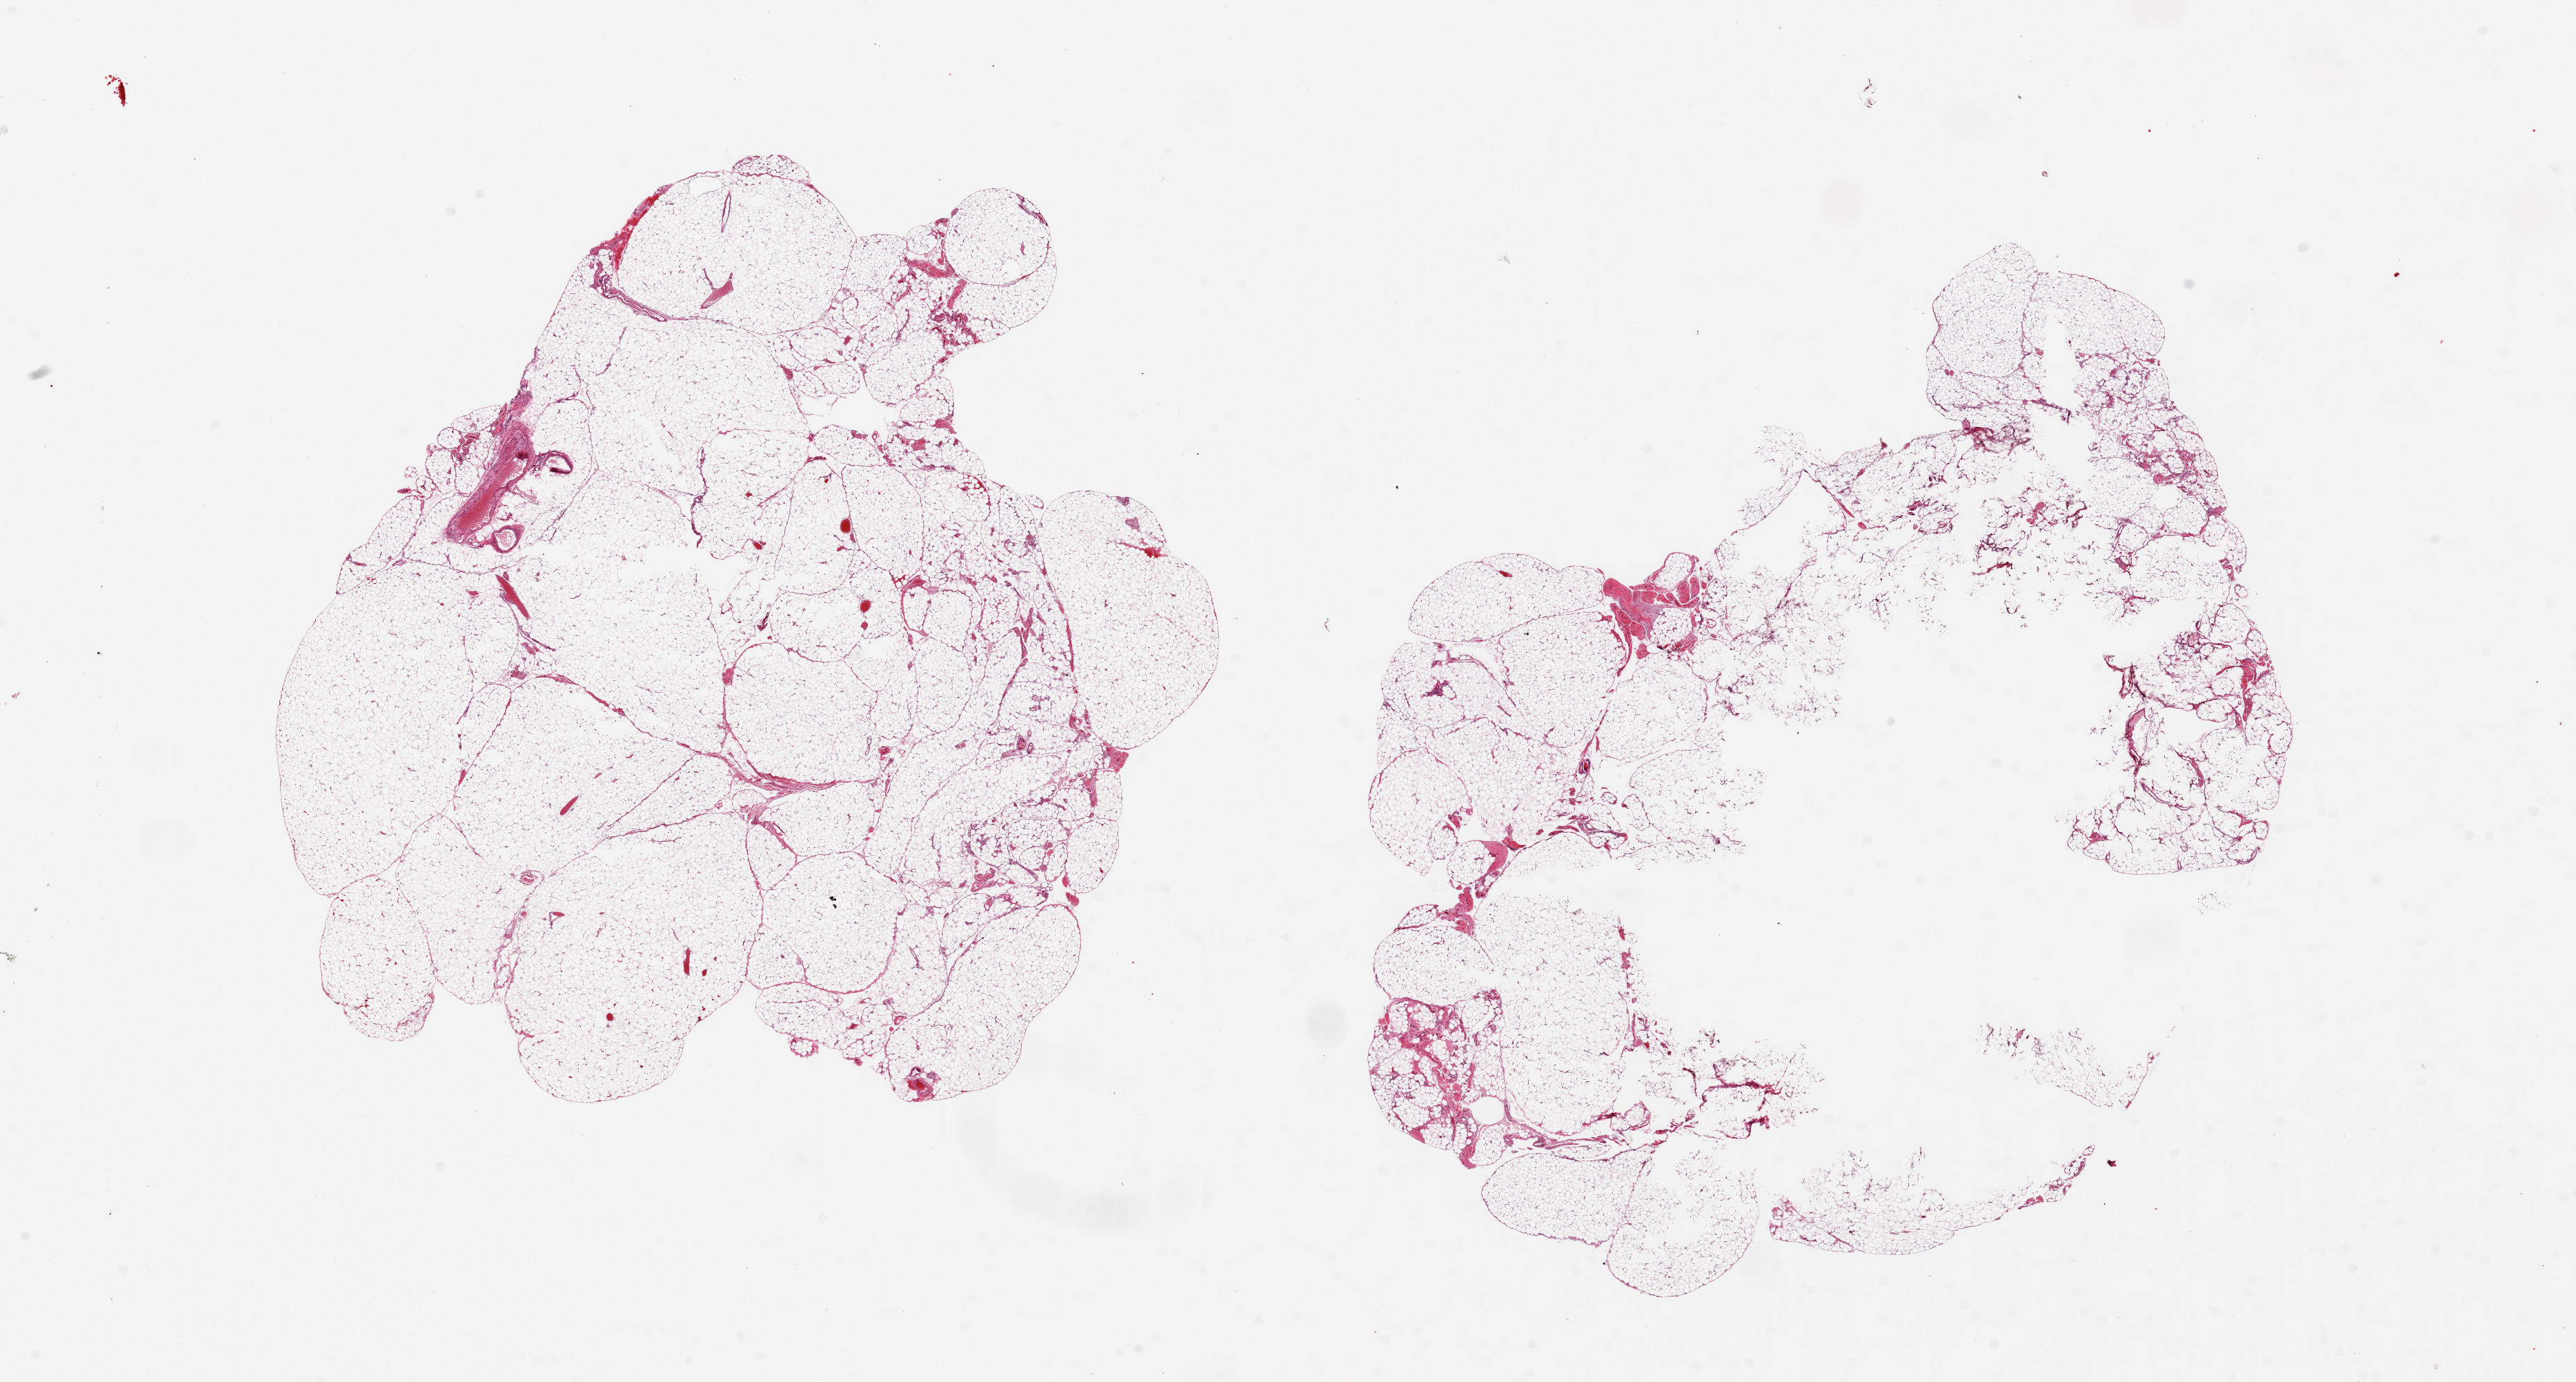
Whole-slide image, hematoxylin and eosin (H&E) stain, brightfield, low-resolution overview of the scanned area, about 29.5 x 15.8 mm. PAXgene-fixed paraffin-embedded (PFPE) section. Section of omentum (target tissue). Donor tissue sample. Donor: female.
* review note (as recorded): 2 pieces, 12x8 & 12x10mm; 1 with large 6 mm central hole; 1 without defects